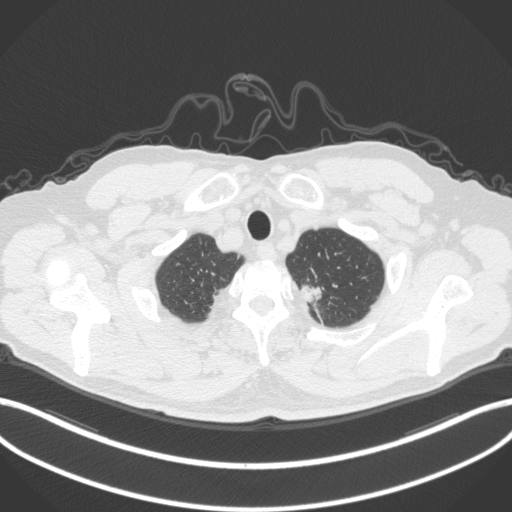
Chest CT, one axial slice; slice 348 of 382 in the series (ordered by position); reconstruction kernel B31f; 120 kVp; lung window (W 1500 / L -600 HU); 1 mm slice thickness; 512 × 512 image matrix. Male patient, age 64 years. From the clinical record (not read from this slice): clinical TNM (as recorded): T1c N0 M0.
Structures marked on this image (bounding box drawn by a radiologist):
- lung tumour (recorded histology: adenocarcinoma): bounding box [x1, y1, x2, y2] px = [303, 278, 330, 308]